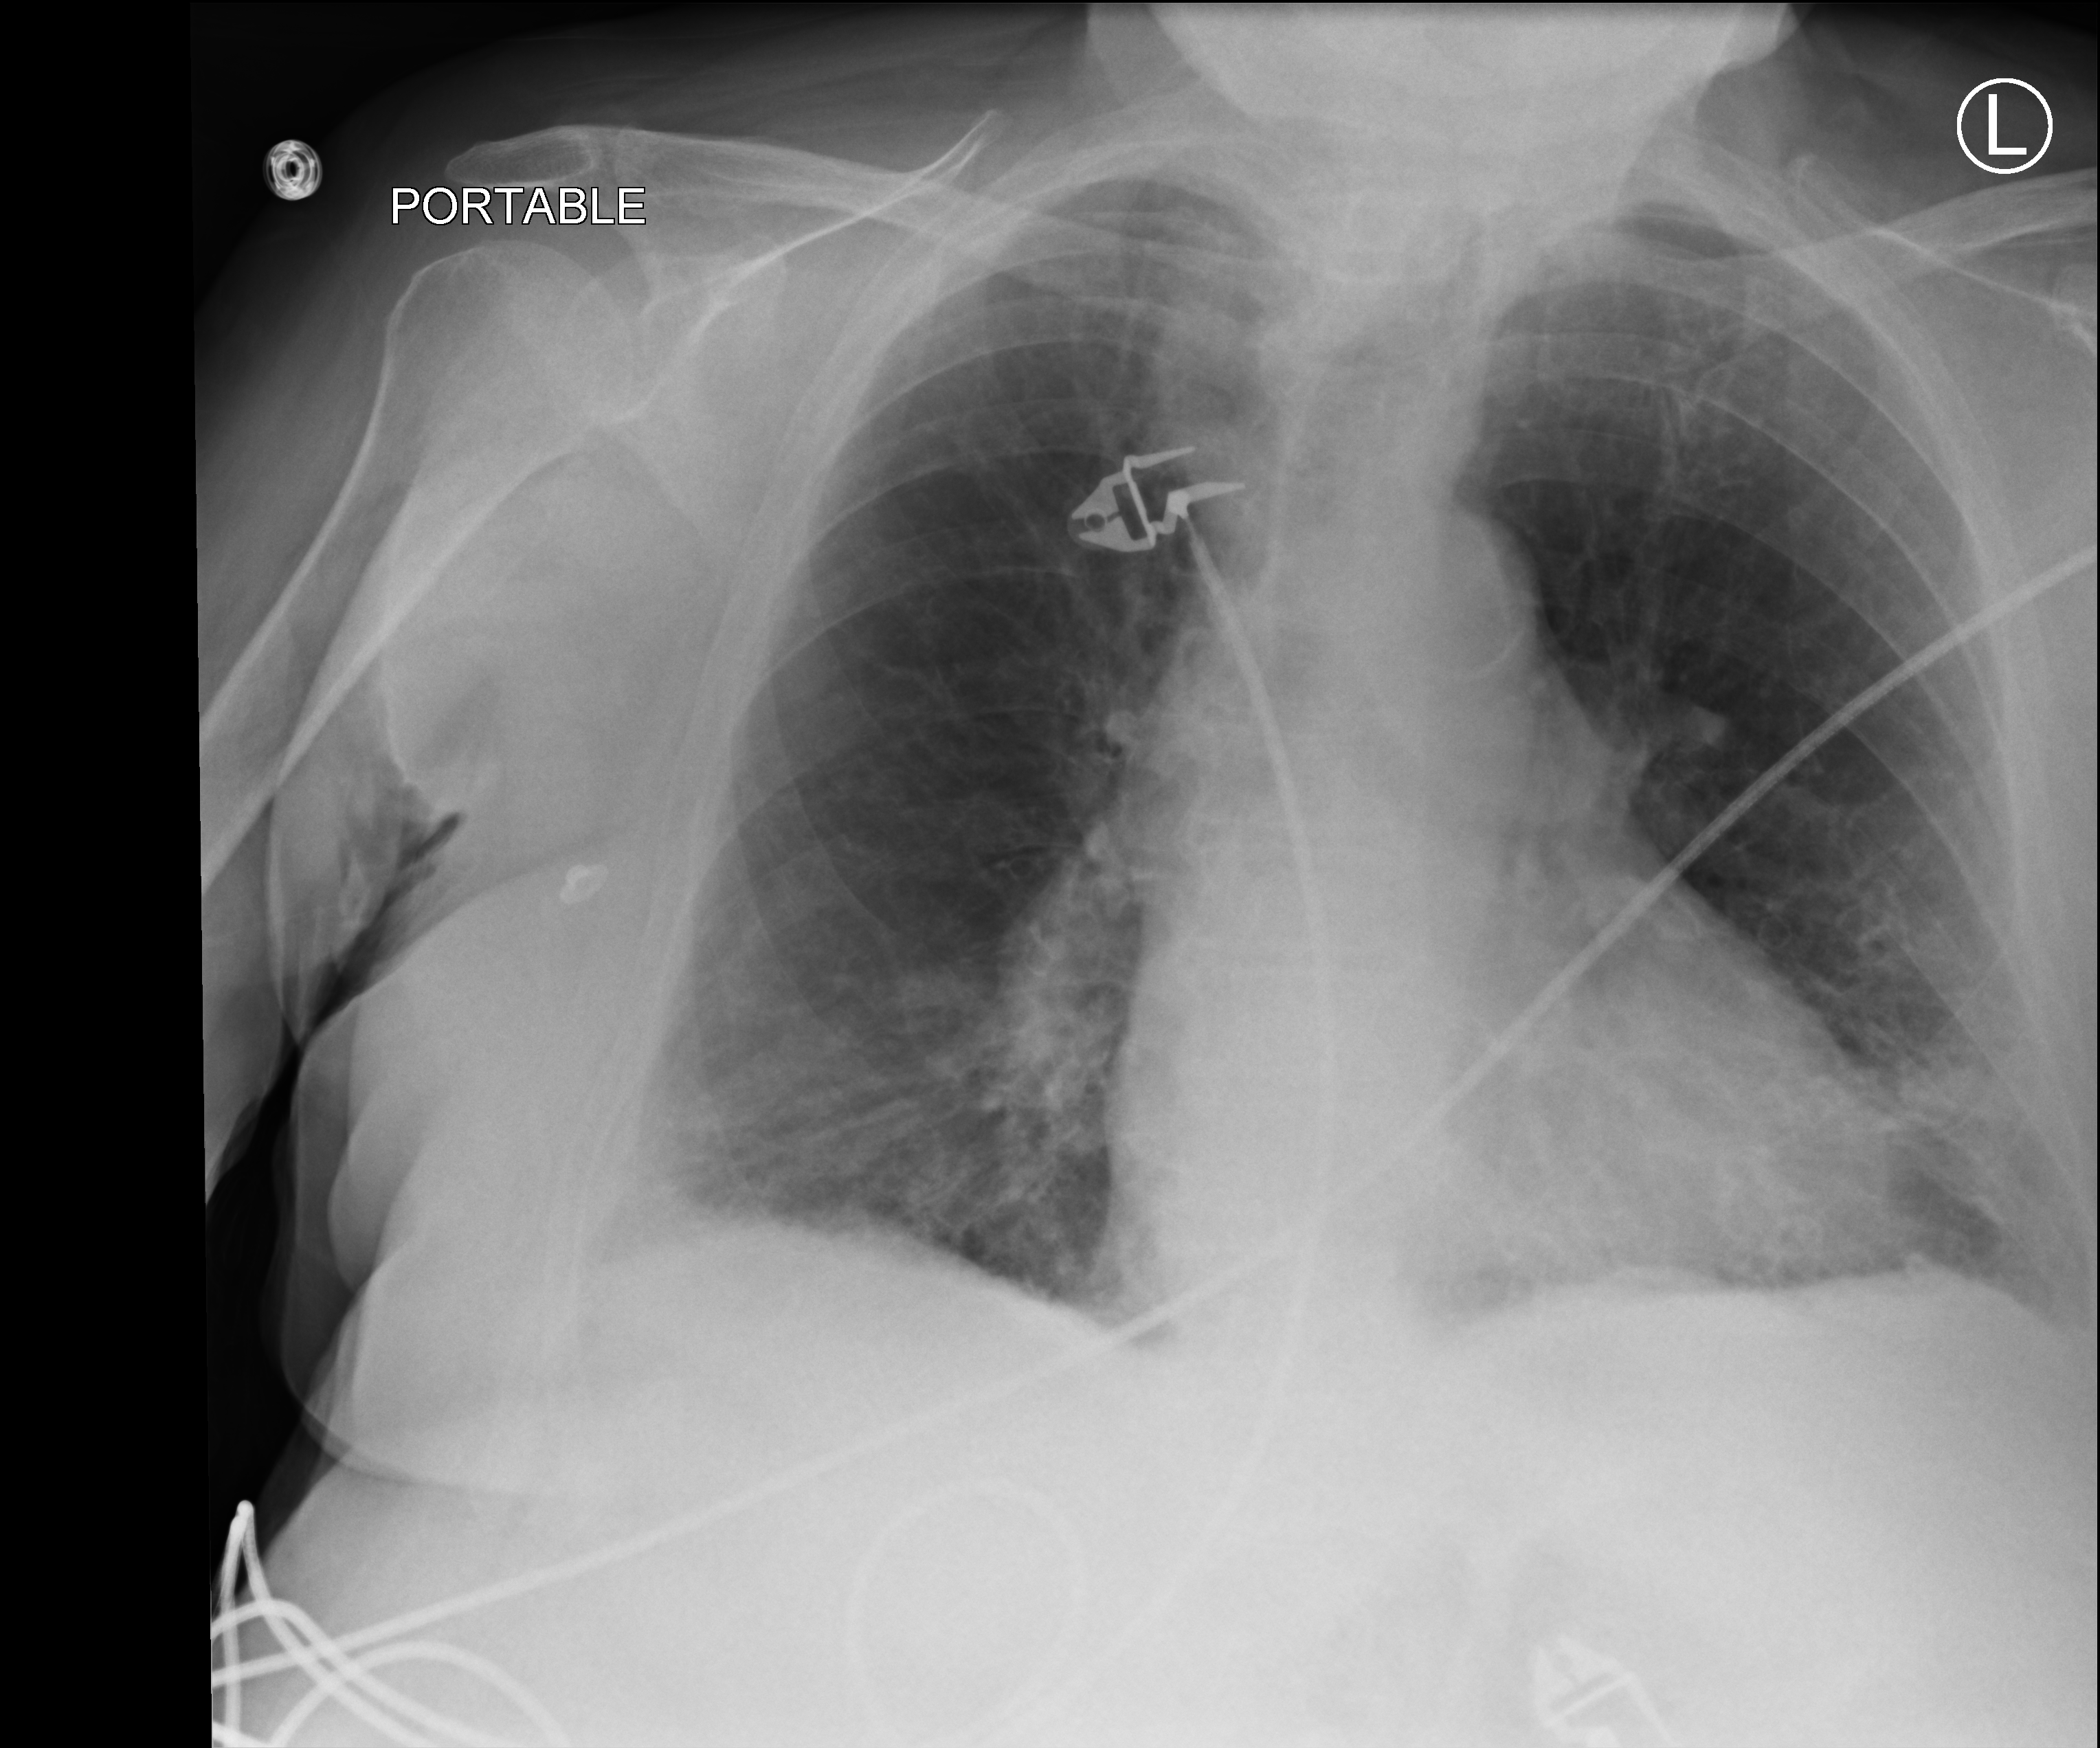
Bedside chest radiograph (computed radiography); anteroposterior (AP) projection. Patient hospitalised with COVID-19; female, aged 75–90 years.
Admission-level facts for this patient (not findings on this image; timing relative to this image not recorded): smoking status (admission record): former.